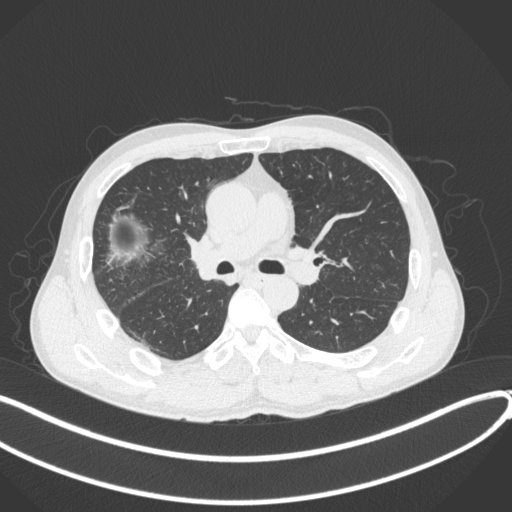
Chest CT, one axial slice; slice 231 of 409 in the series (ordered by position); 120 kVp; lung window (W 1500 / L -600 HU); 1 mm slice thickness; 512 × 512 image matrix. Patient: male, 53 years. From the clinical record (not read from this slice): clinical TNM (as recorded): T1b N0 M0.
Annotated regions visible in this slice (rectangle marked by the reading radiologist):
- lung tumour (recorded histology: squamous cell carcinoma): bounding box (x1, y1, x2, y2) in pixels: (186, 231, 225, 288)